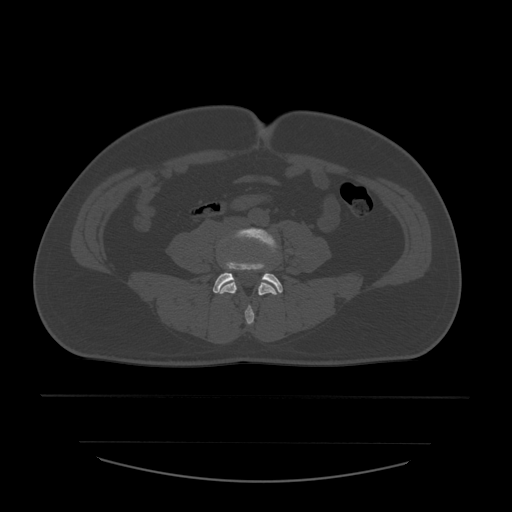
CT including the spine, one axial slice; slice 134 of 532 in the series (ordered by position); 120 kVp; bone window (W 1800 / L 400 HU); 1.25 mm slice thickness; 512 × 512 image matrix. Patient age 44 years. From the clinical record (not read from this slice): primary cancer: soft tissue sarcoma.
Structures marked on this image (semi-automatic segmentation, software-assisted and operator-edited):
- L4 vertebra: bounding box [x1, y1, x2, y2] px = [220, 228, 279, 325]
- L5 vertebra: [213, 262, 283, 293]